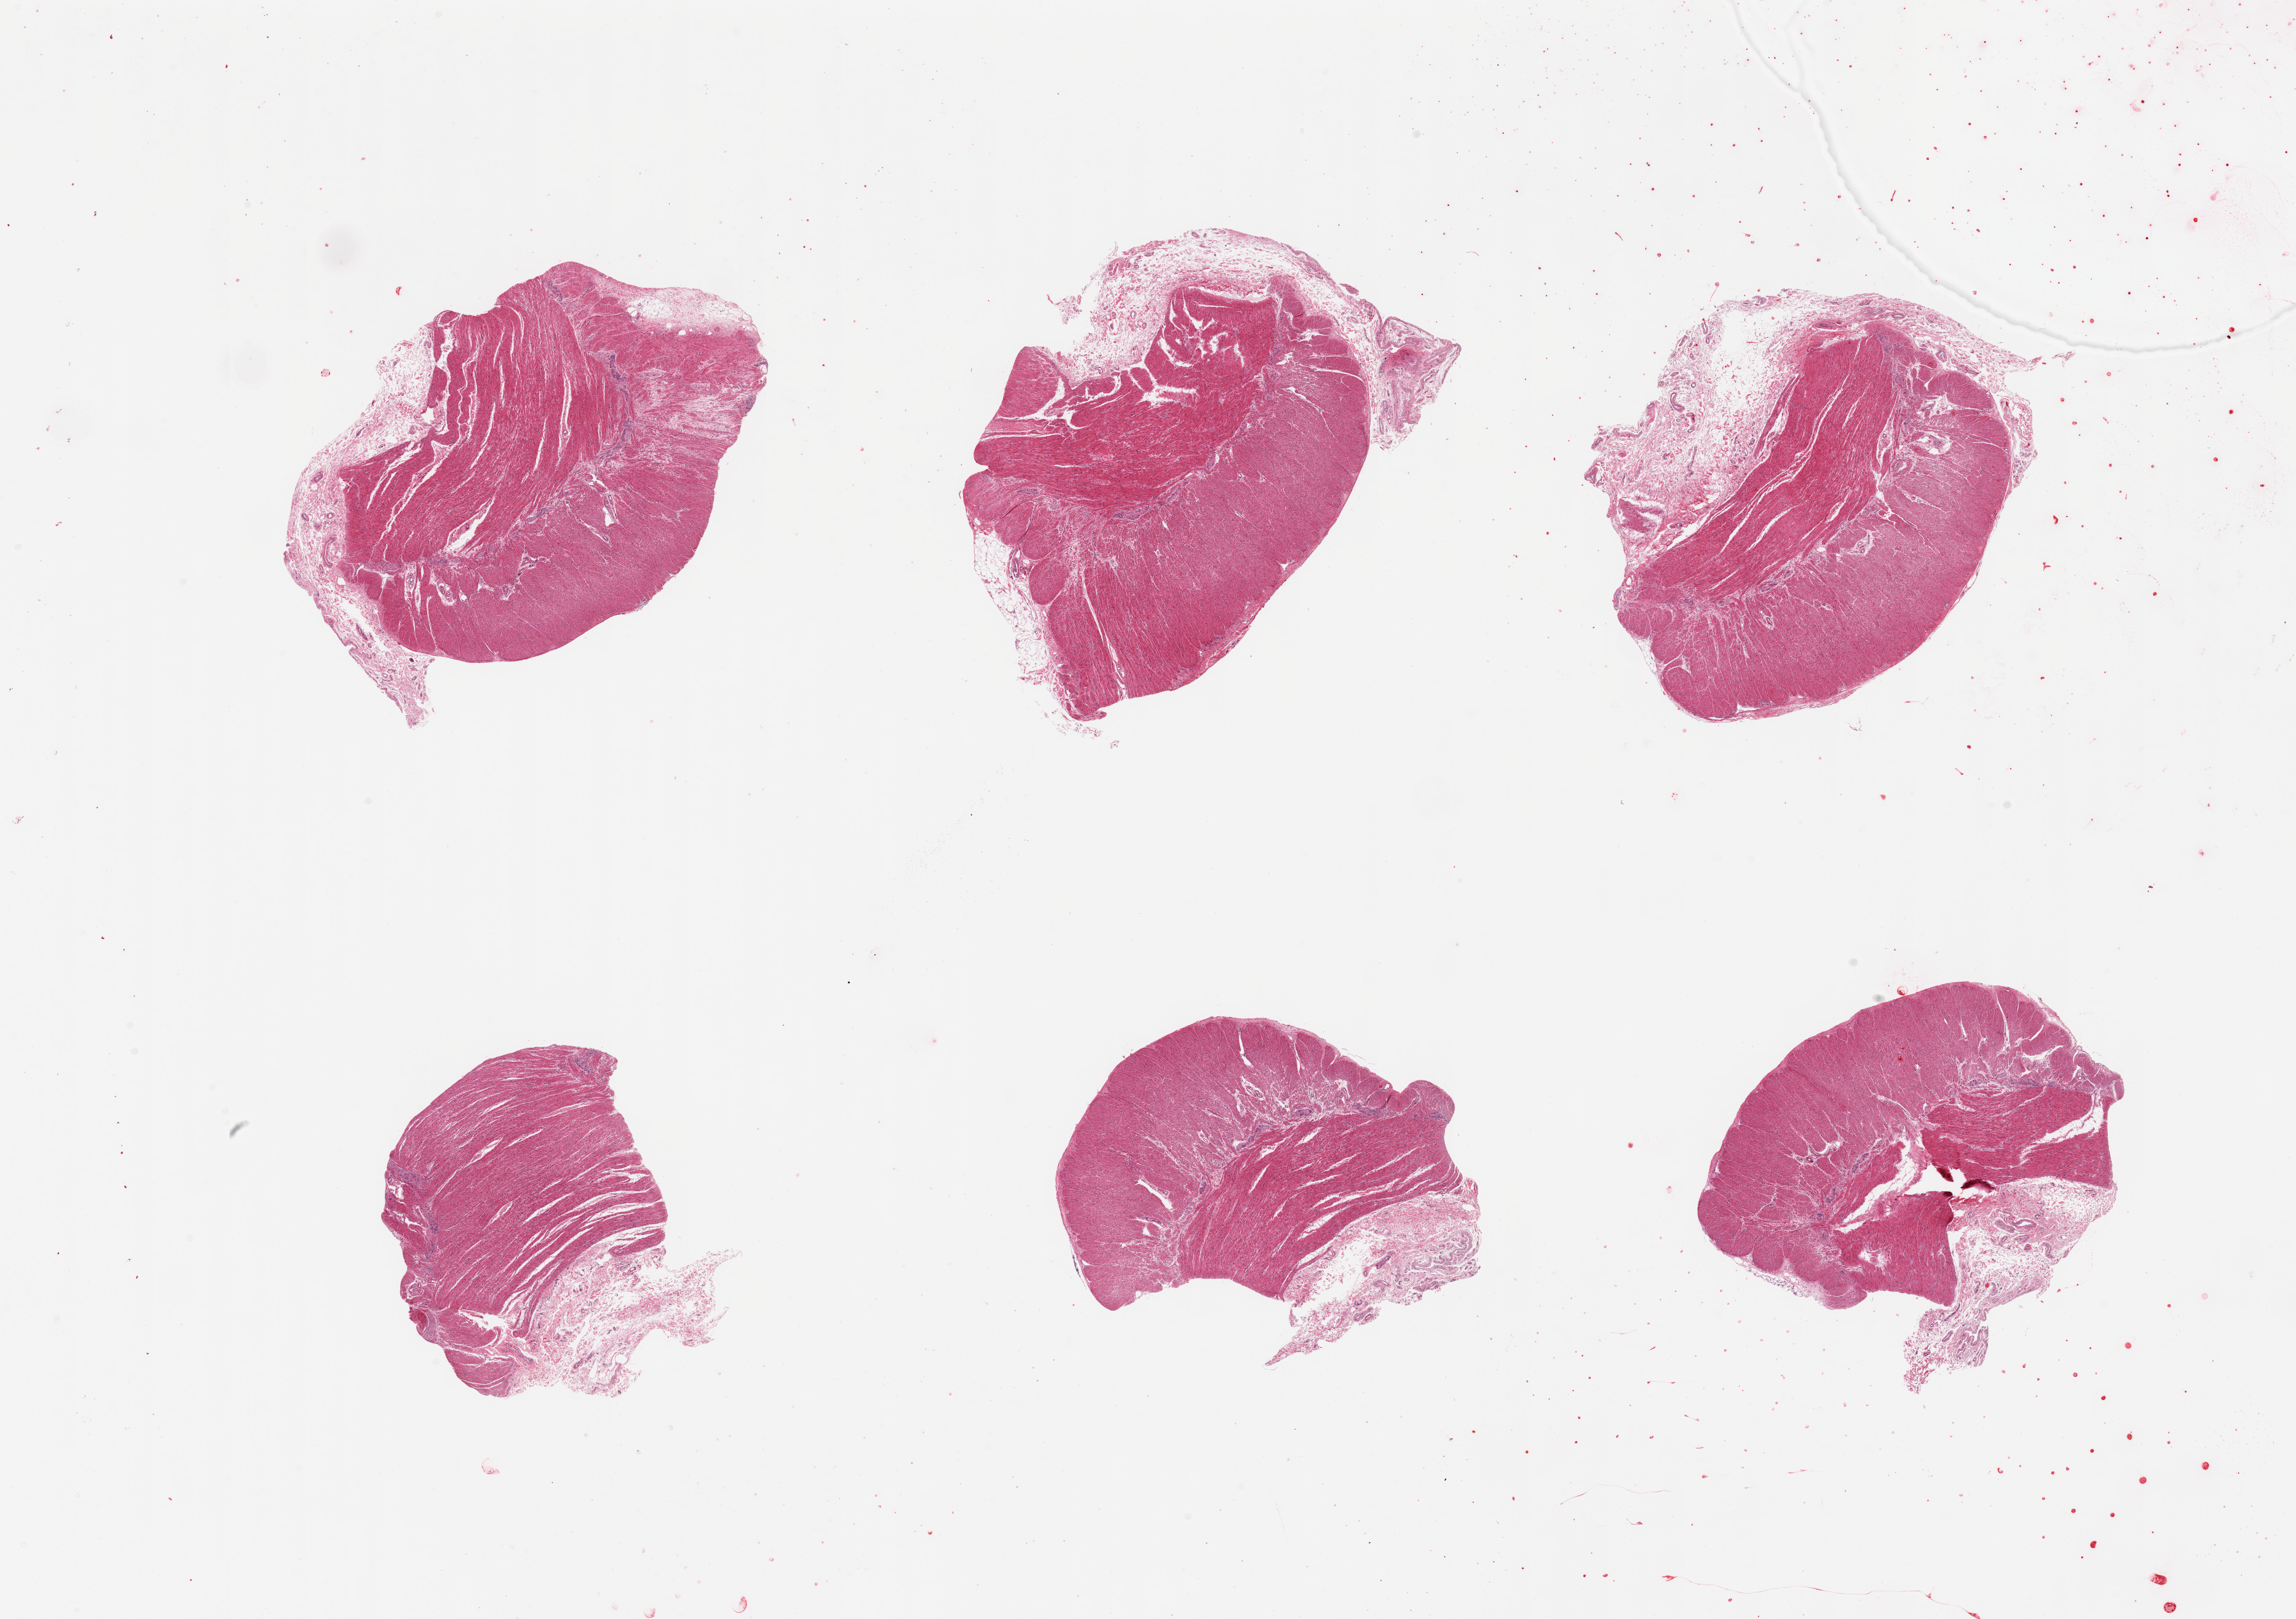
Digitized H&E-stained section — shown as a low-resolution overview of the whole scanned area (about 29.5 x 20.8 mm). Male donor.
- specimen: PAXgene-fixed paraffin-embedded (PFPE) section; target tissue: sigmoid colon; tissue donor sample